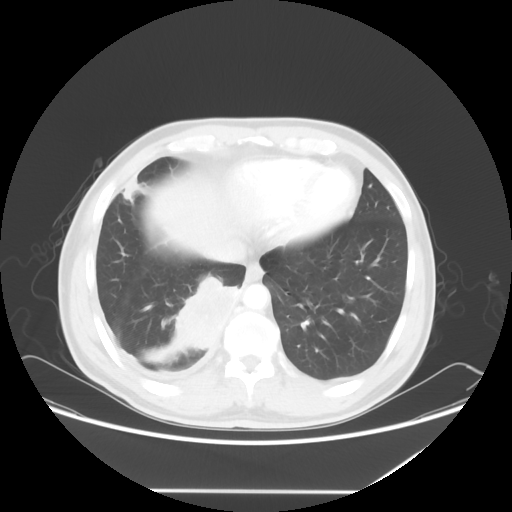
Chest CT, one axial slice. Reconstruction kernel STANDARD. 120 kVp. Lung window (W 1500 / L -600 HU). 512 × 512 image matrix, field of view 419 × 419 mm. Patient: male, 48 years. Case-level facts recorded for this patient, not image findings: clinical TNM (as recorded): T3 N3 M1a.
Annotated regions visible in this slice (bounding box drawn by a radiologist):
- lung tumour (recorded histology: squamous cell carcinoma): box from (x=168, y=265) to (x=241, y=353) px